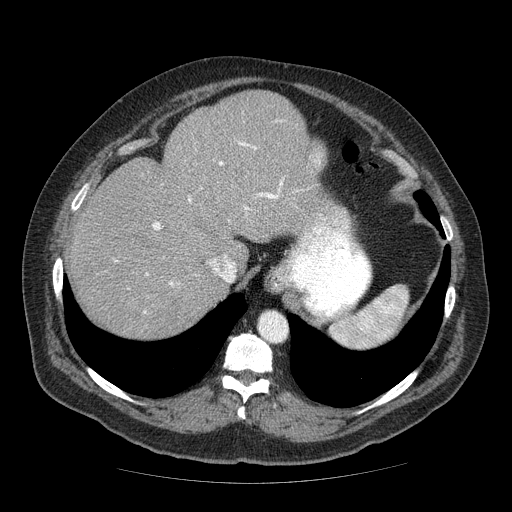
Contrast-enhanced abdominal CT (liver protocol), one axial slice; slice 50 of 85 in the series (ordered by position); reconstruction kernel STANDARD; soft-tissue window (W 400 / L 40 HU); 2.5 mm slice thickness; 512 × 512 image matrix. From the clinical record (not read from this slice): diagnosis: hepatocellular carcinoma (patient treated with transarterial chemoembolisation; whether this scan precedes or follows treatment is not stated here); TNM stage (as recorded): Stage-IIIA; Child-Pugh class: A; tumour nodularity: multinodular; tumour size: 7 cm.
Structures marked on this image (semi-automatically segmented with operator editing):
- abdominal aorta: box from (x=258, y=312) to (x=287, y=342) px
- liver parenchyma outside the tumour (the mass and vessels are separate outlines, so this box may not span the whole liver): (x=66, y=90)–(x=348, y=338)
- liver vessels: (x=115, y=120)–(x=344, y=313)